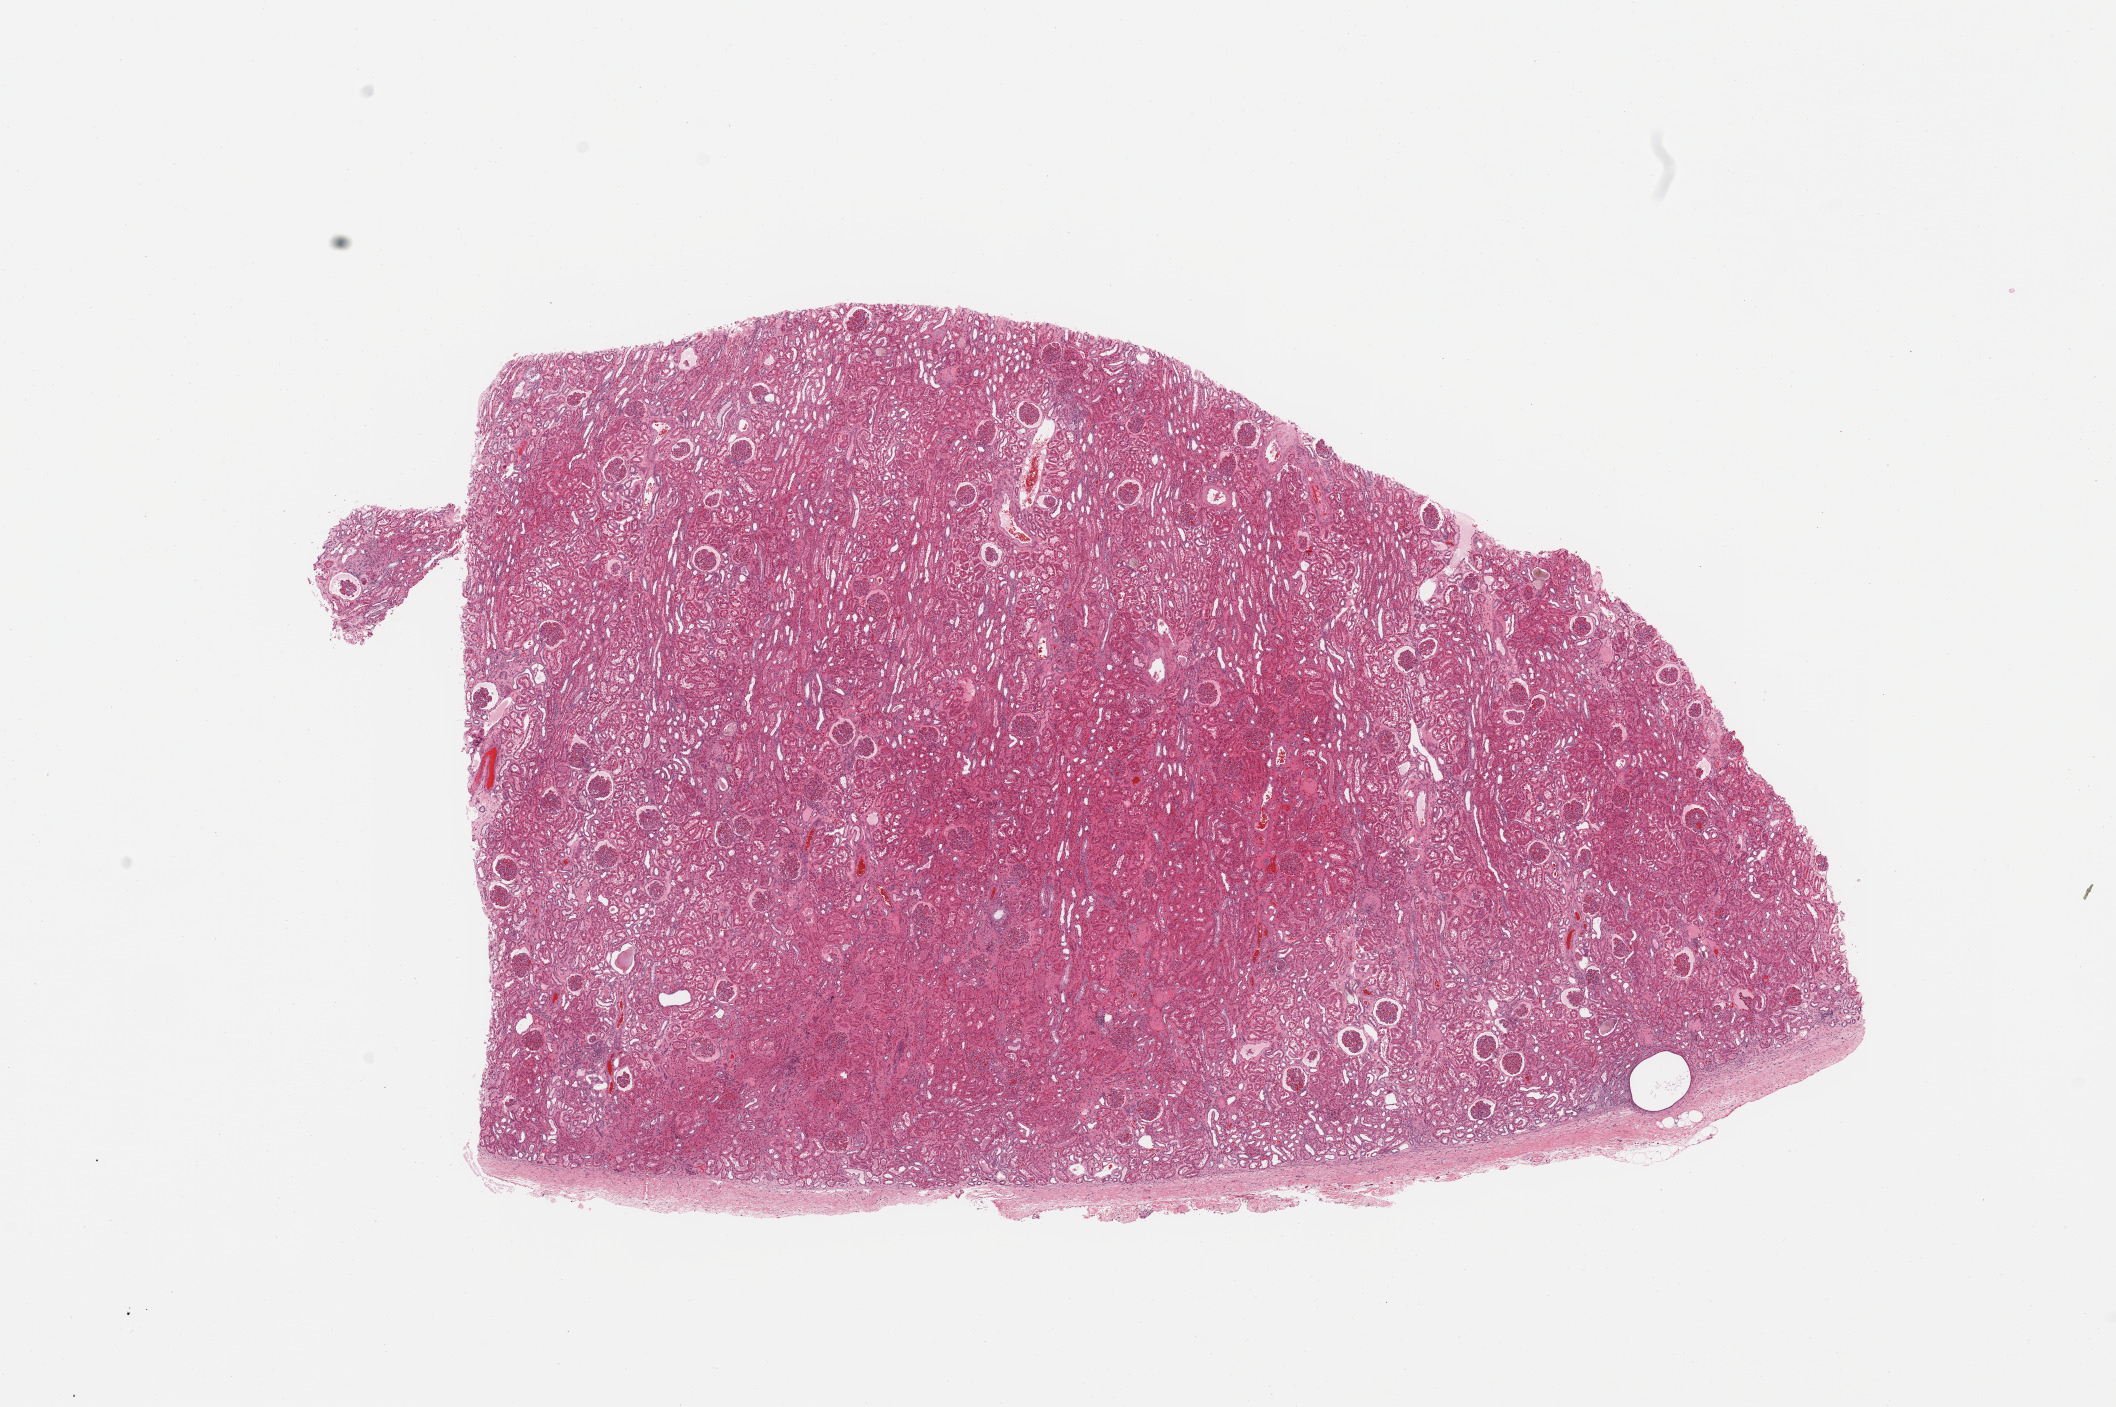
Whole-slide histology image, H&E-stained — low-resolution overview of the scanned area, about 16.7 x 11.1 mm (acquisition: 20x scan); normal (non-tumour) tissue sample, sampled site: kidney. 63-year-old male patient.
• this section: normal (non-tumour) tissue from the same patient
• patient diagnosis: Renal cell carcinoma, NOS